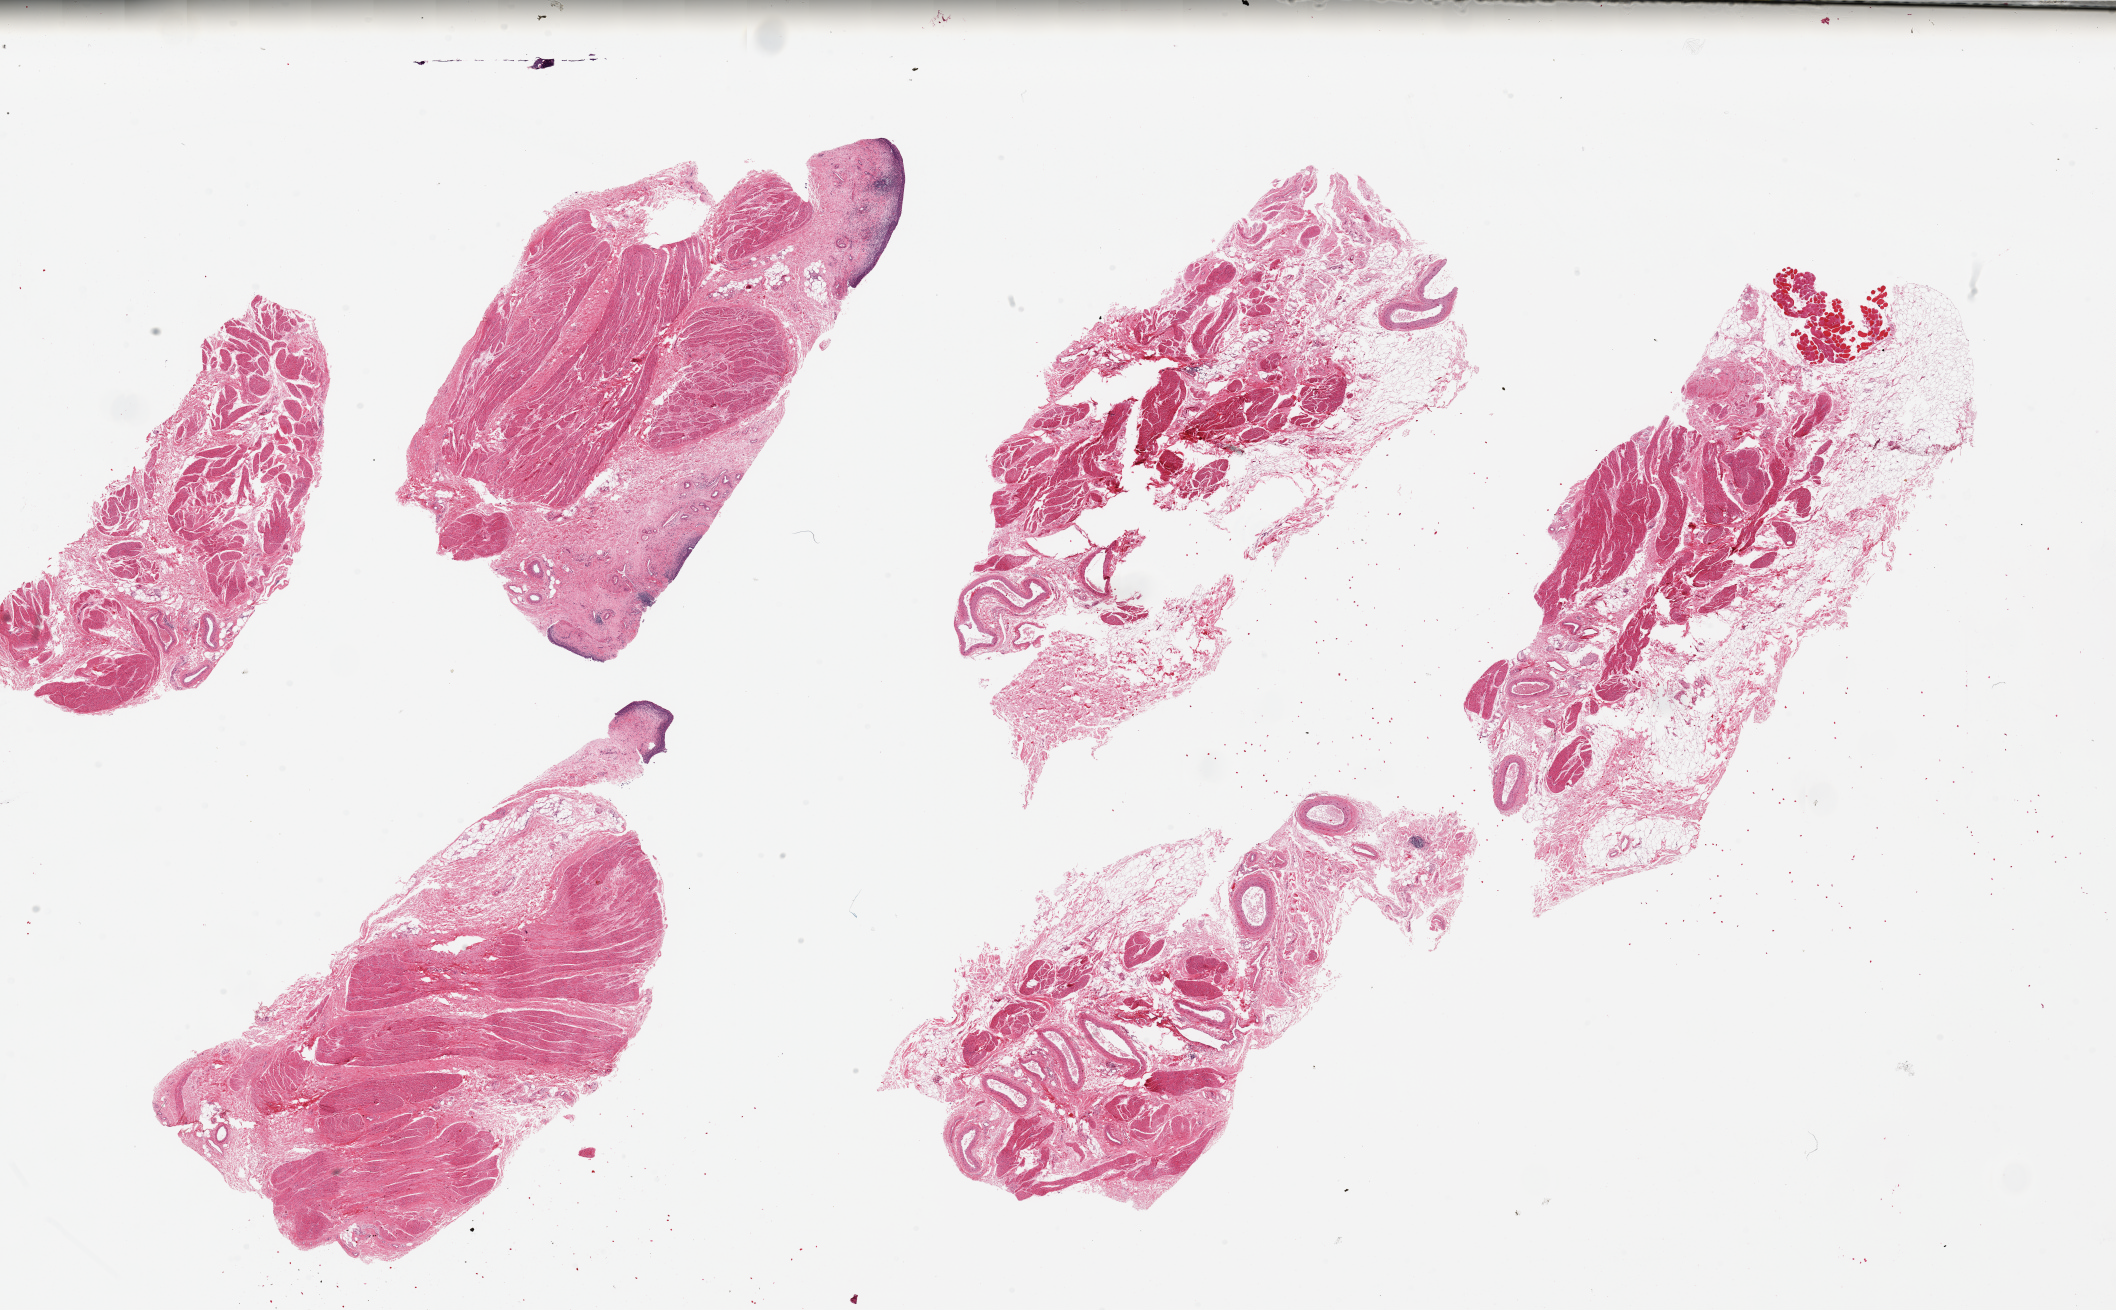
Whole-slide image, hematoxylin and eosin (H&E) stain, brightfield, a low-resolution overview of the entire scanned area, about 33.5 x 20.7 mm (slide scanned at 20x), PAXgene-fixed paraffin-embedded (PFPE) section, target tissue: urinary bladder, tissue donor sample. Male donor.
Pathologist's review note for this sample: 6 pieces up to 9x4.8 mm; little mucosa sampled; mild chronic inflammation.